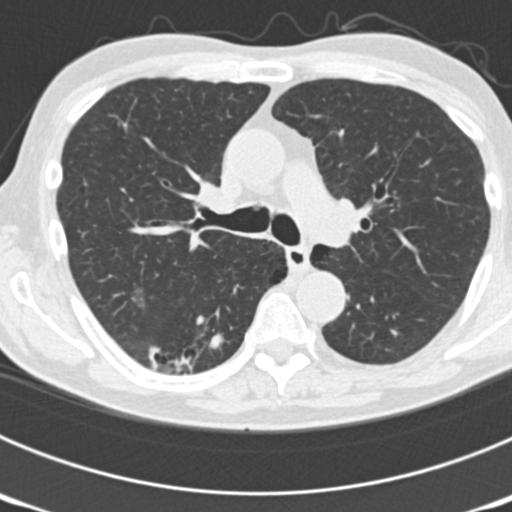
Low-dose screening chest CT, one axial slice. Slice 118 of 177 in the series (ordered by position). Reconstruction kernel B30f. 120 kVp. Lung window (W 1500 / L -600 HU). 512 × 512 image matrix, field of view 300 × 300 mm.
Annotated regions visible in this slice (manually delineated by an expert):
- lesion 6 (nodule, lower lobe of right lung): bounding box (x1, y1, x2, y2) in pixels: (207, 333, 225, 350)